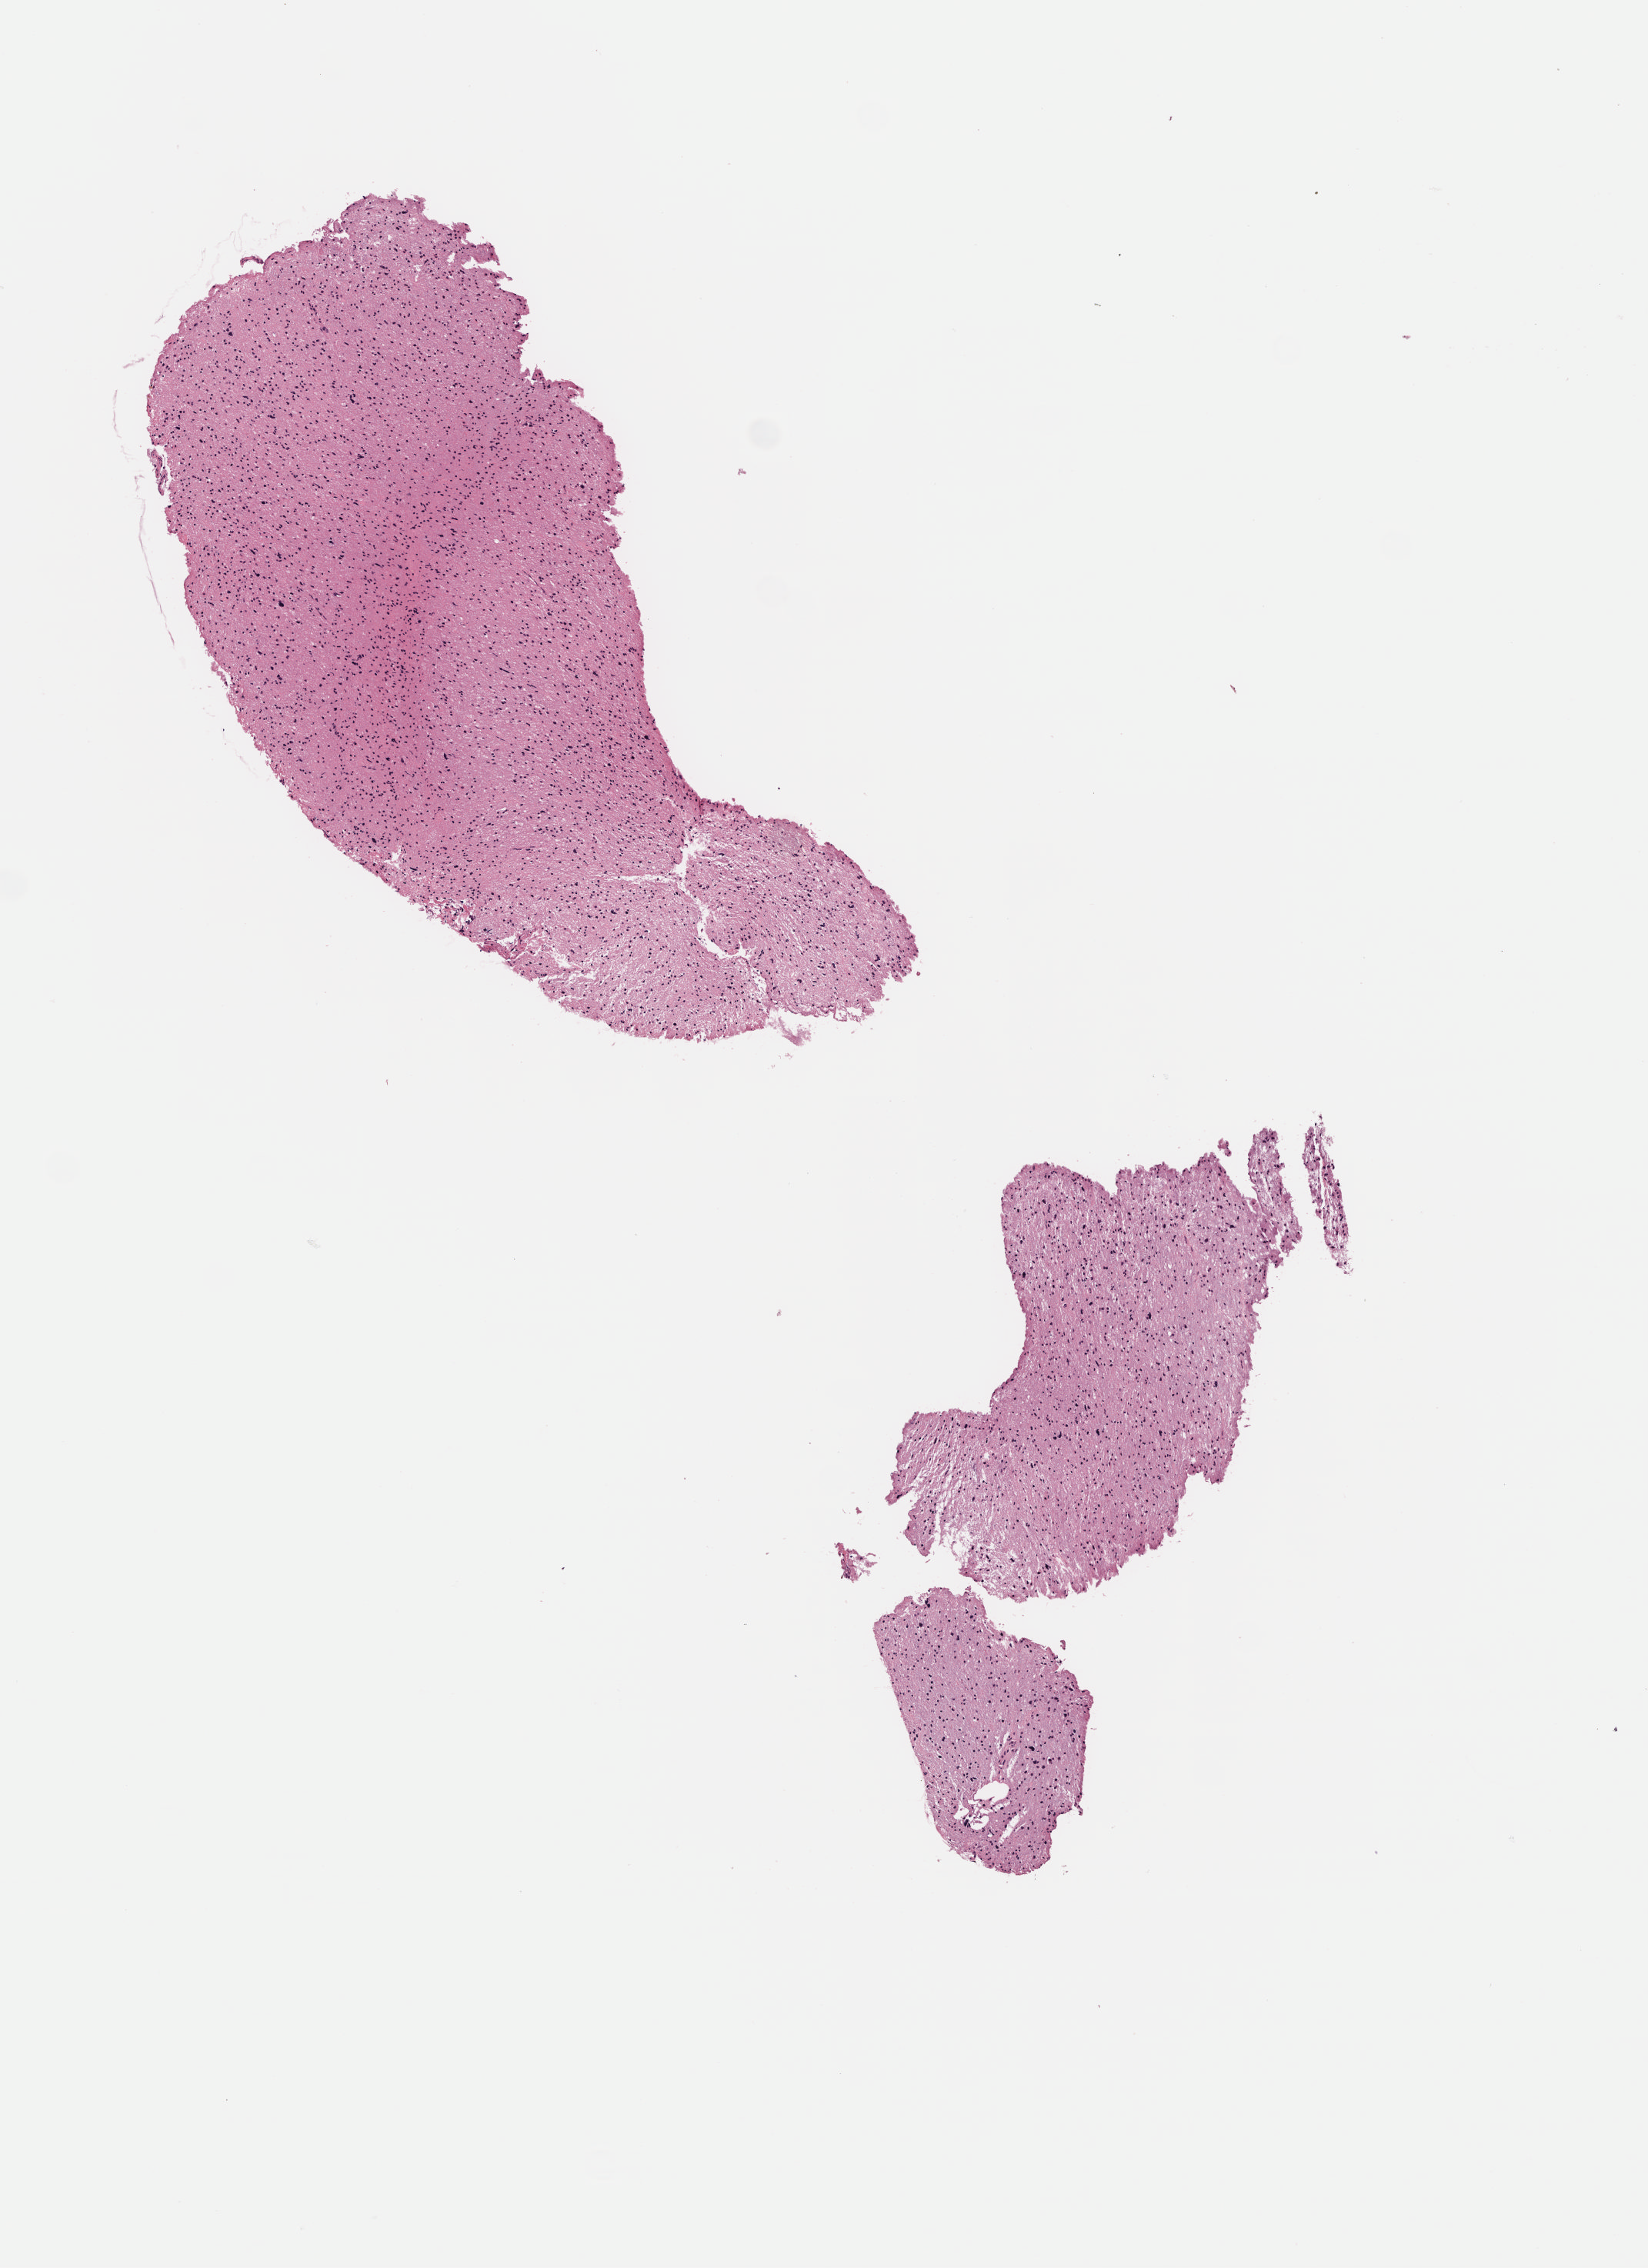
H&E whole-slide image, low-resolution overview of the scanned area, about 4.2 x 5.8 mm (slide scanned at 40x), FFPE section, sample: primary tumour, brain. Male patient; age at initial diagnosis 44 years. Histologic grade: G3 (poorly differentiated).
Diagnosis: Astrocytoma, anaplastic. Laterality: right.